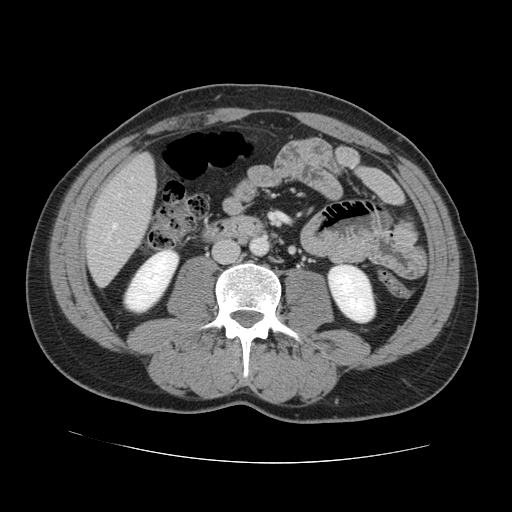
Contrast-enhanced abdominal CT, one axial slice; slice 30 of 131 in the series (ordered by position); intravenous contrast given; soft-tissue window (W 400 / L 40 HU); 2.5 mm slice thickness; 512 × 512 image matrix. Male patient, age 40 years. Case-level facts recorded for this patient, not image findings: diagnosis: colorectal cancer liver metastases, imaged before liver resection; multiple liver metastases: yes; largest metastasis: 2.9 cm; disease in both lobes: yes.
Outlined on this slice (manually delineated by an expert):
- hepatic veins: bounding box (x1, y1, x2, y2) in pixels: (108, 194, 120, 238)
- liver: (87, 155, 155, 284)